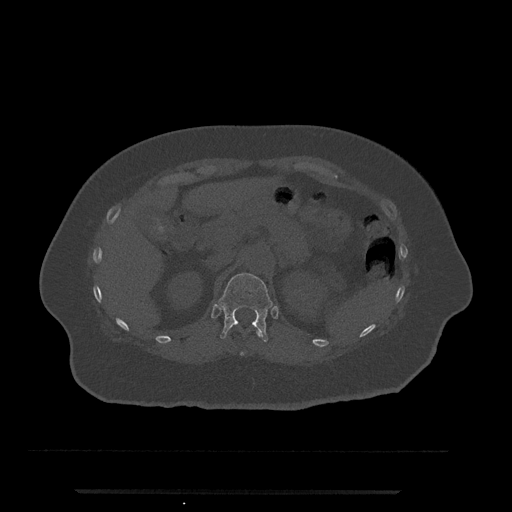
CT including the spine, one axial slice; 120 kVp; bone window (W 1800 / L 400 HU); 0.5 mm slice thickness; 512 × 512 image matrix. Patient: female, 51 years. Case-level facts recorded for this patient, not image findings: primary cancer: neuro.
Structures marked on this image (semi-automatic segmentation, software-assisted and operator-edited):
- T11 vertebra: bounding box (x1, y1, x2, y2) in pixels: (240, 330, 261, 356)
- T12 vertebra: (218, 273, 273, 342)